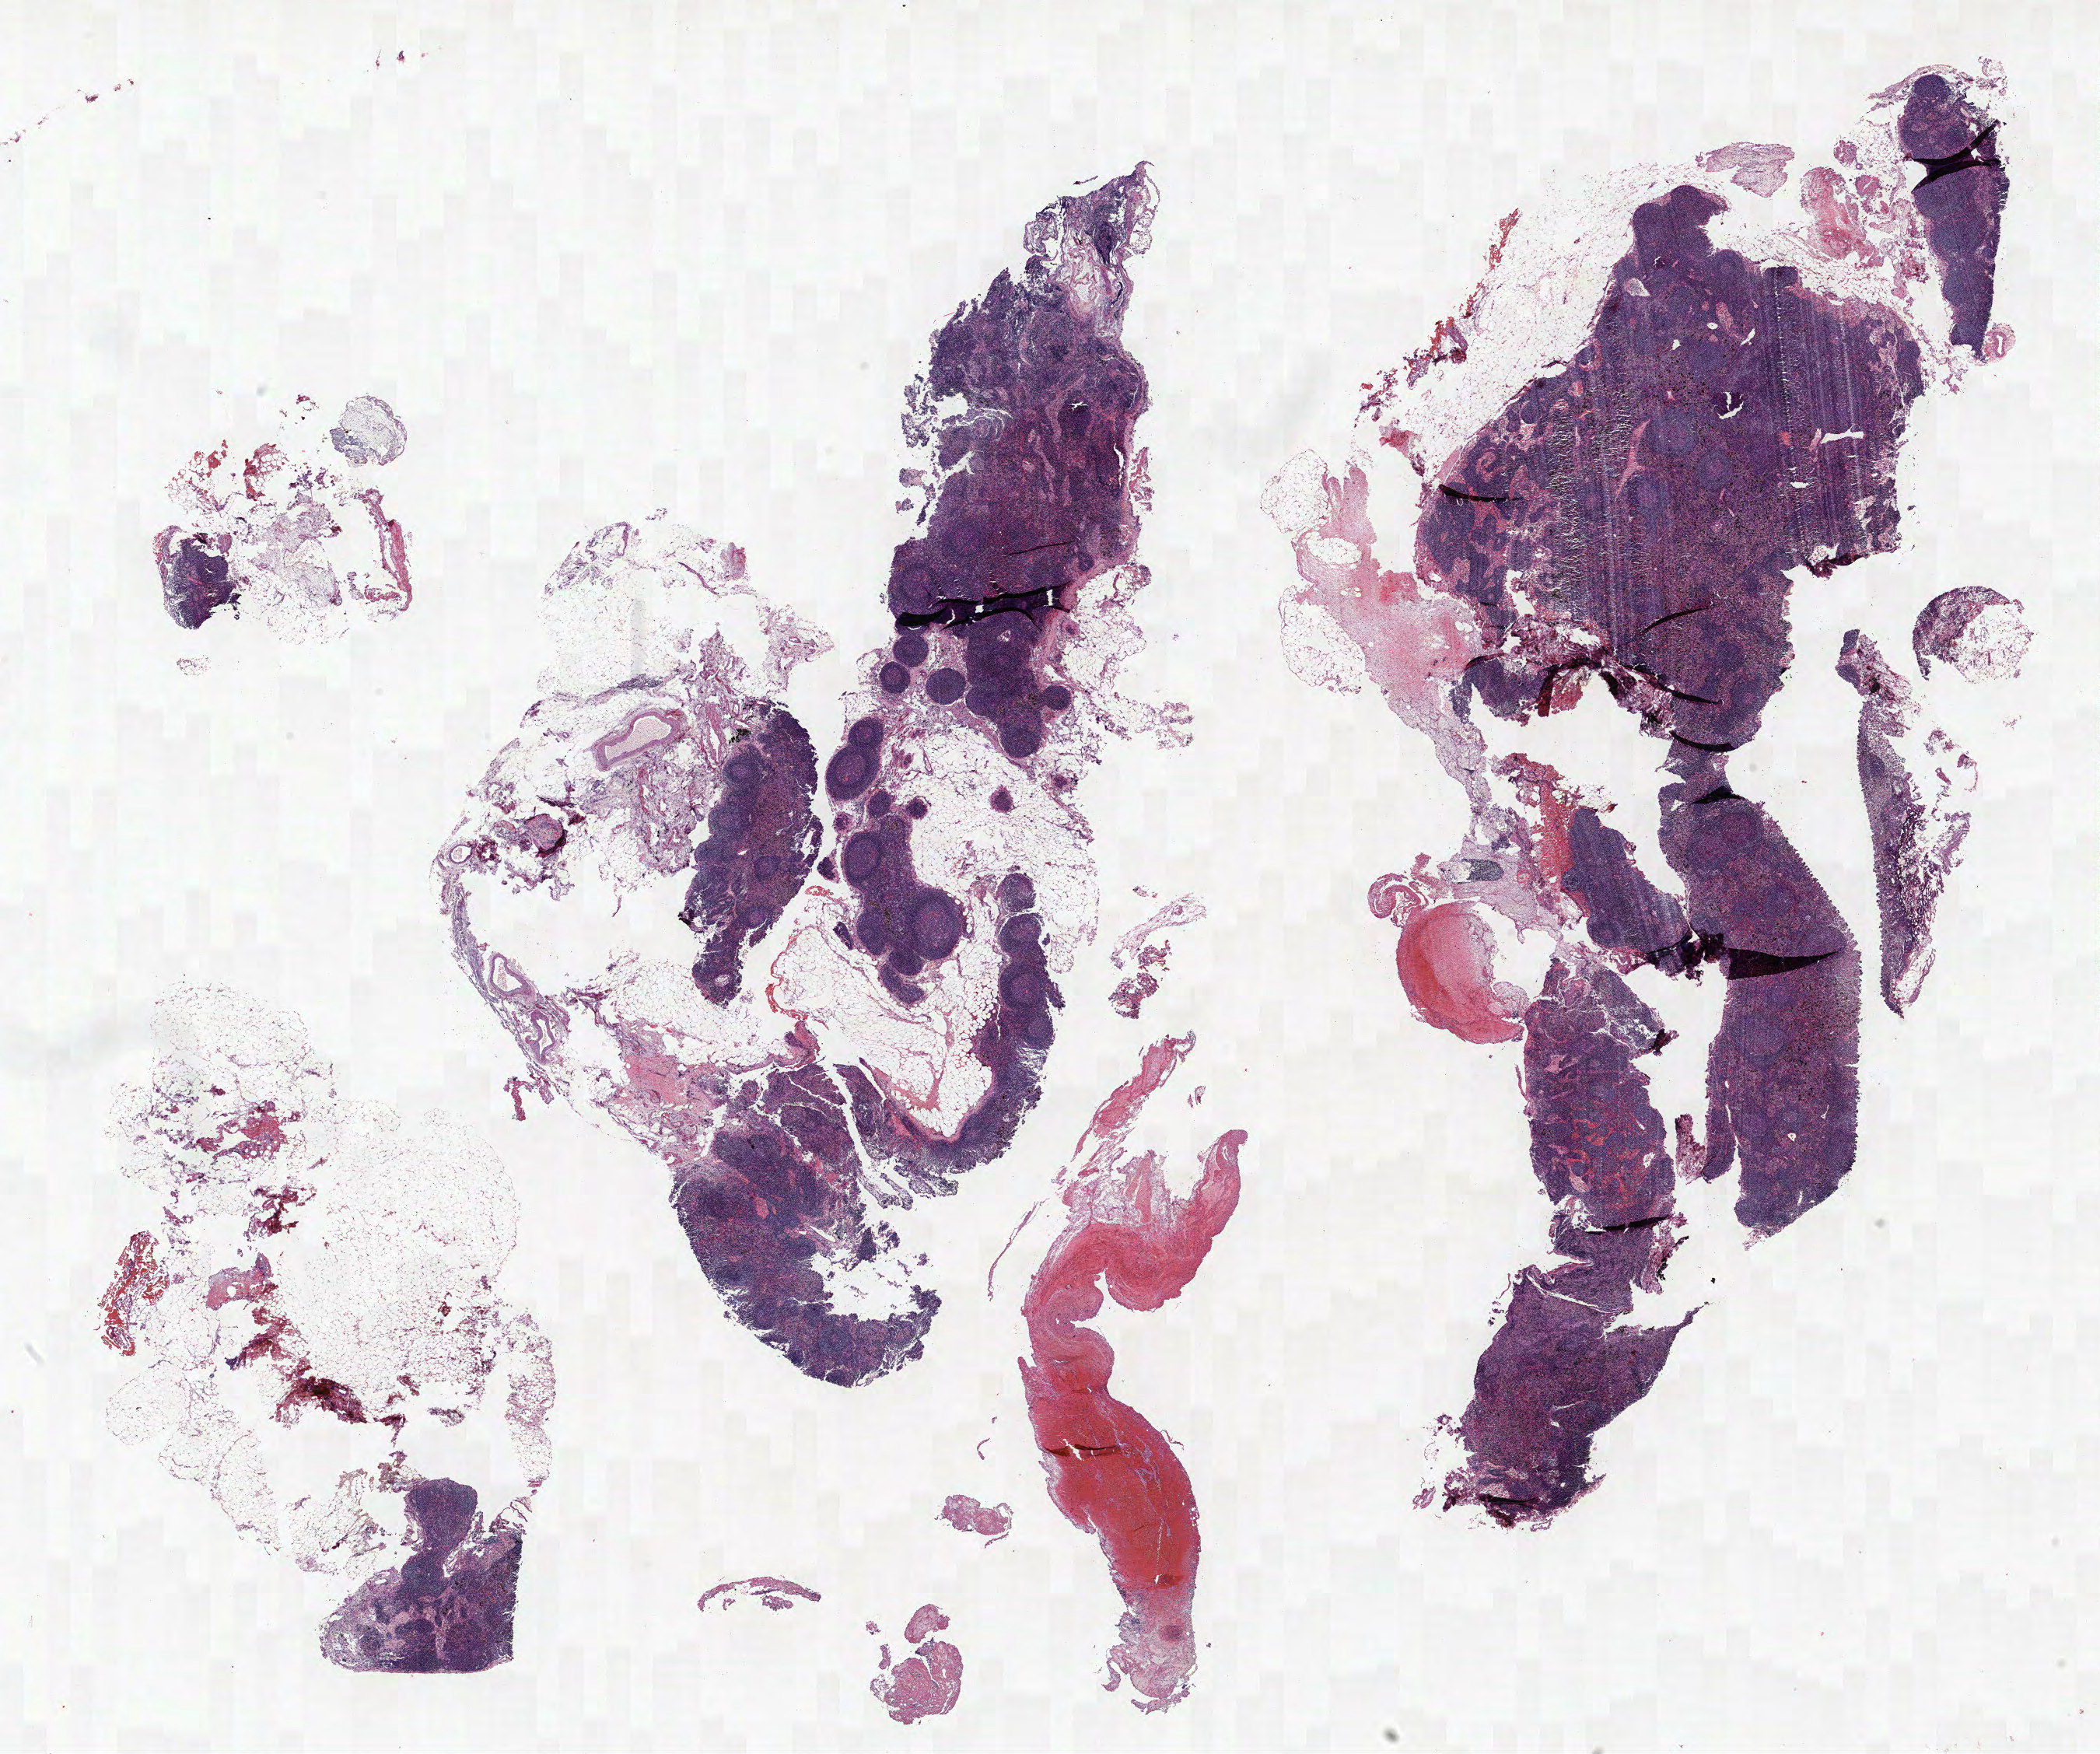
H&E whole-slide image — whole scanned area (about 21.6 x 18.0 mm) shown as a low-resolution overview. Formalin-fixed paraffin-embedded (FFPE) section. Lung tissue. Female, age 66 at enrolment. Current smoker at enrolment. Grade: moderately differentiated (G2).
Primary tumour location (clinical record): right lower lobe. ICD-O-3 topography: lower lobe of lung (C34.3). Stage (AJCC 6th edition): IIA. Participant's lung-cancer diagnosis: Adenocarcinoma, NOS. Tumour size (pathology): 11 mm.